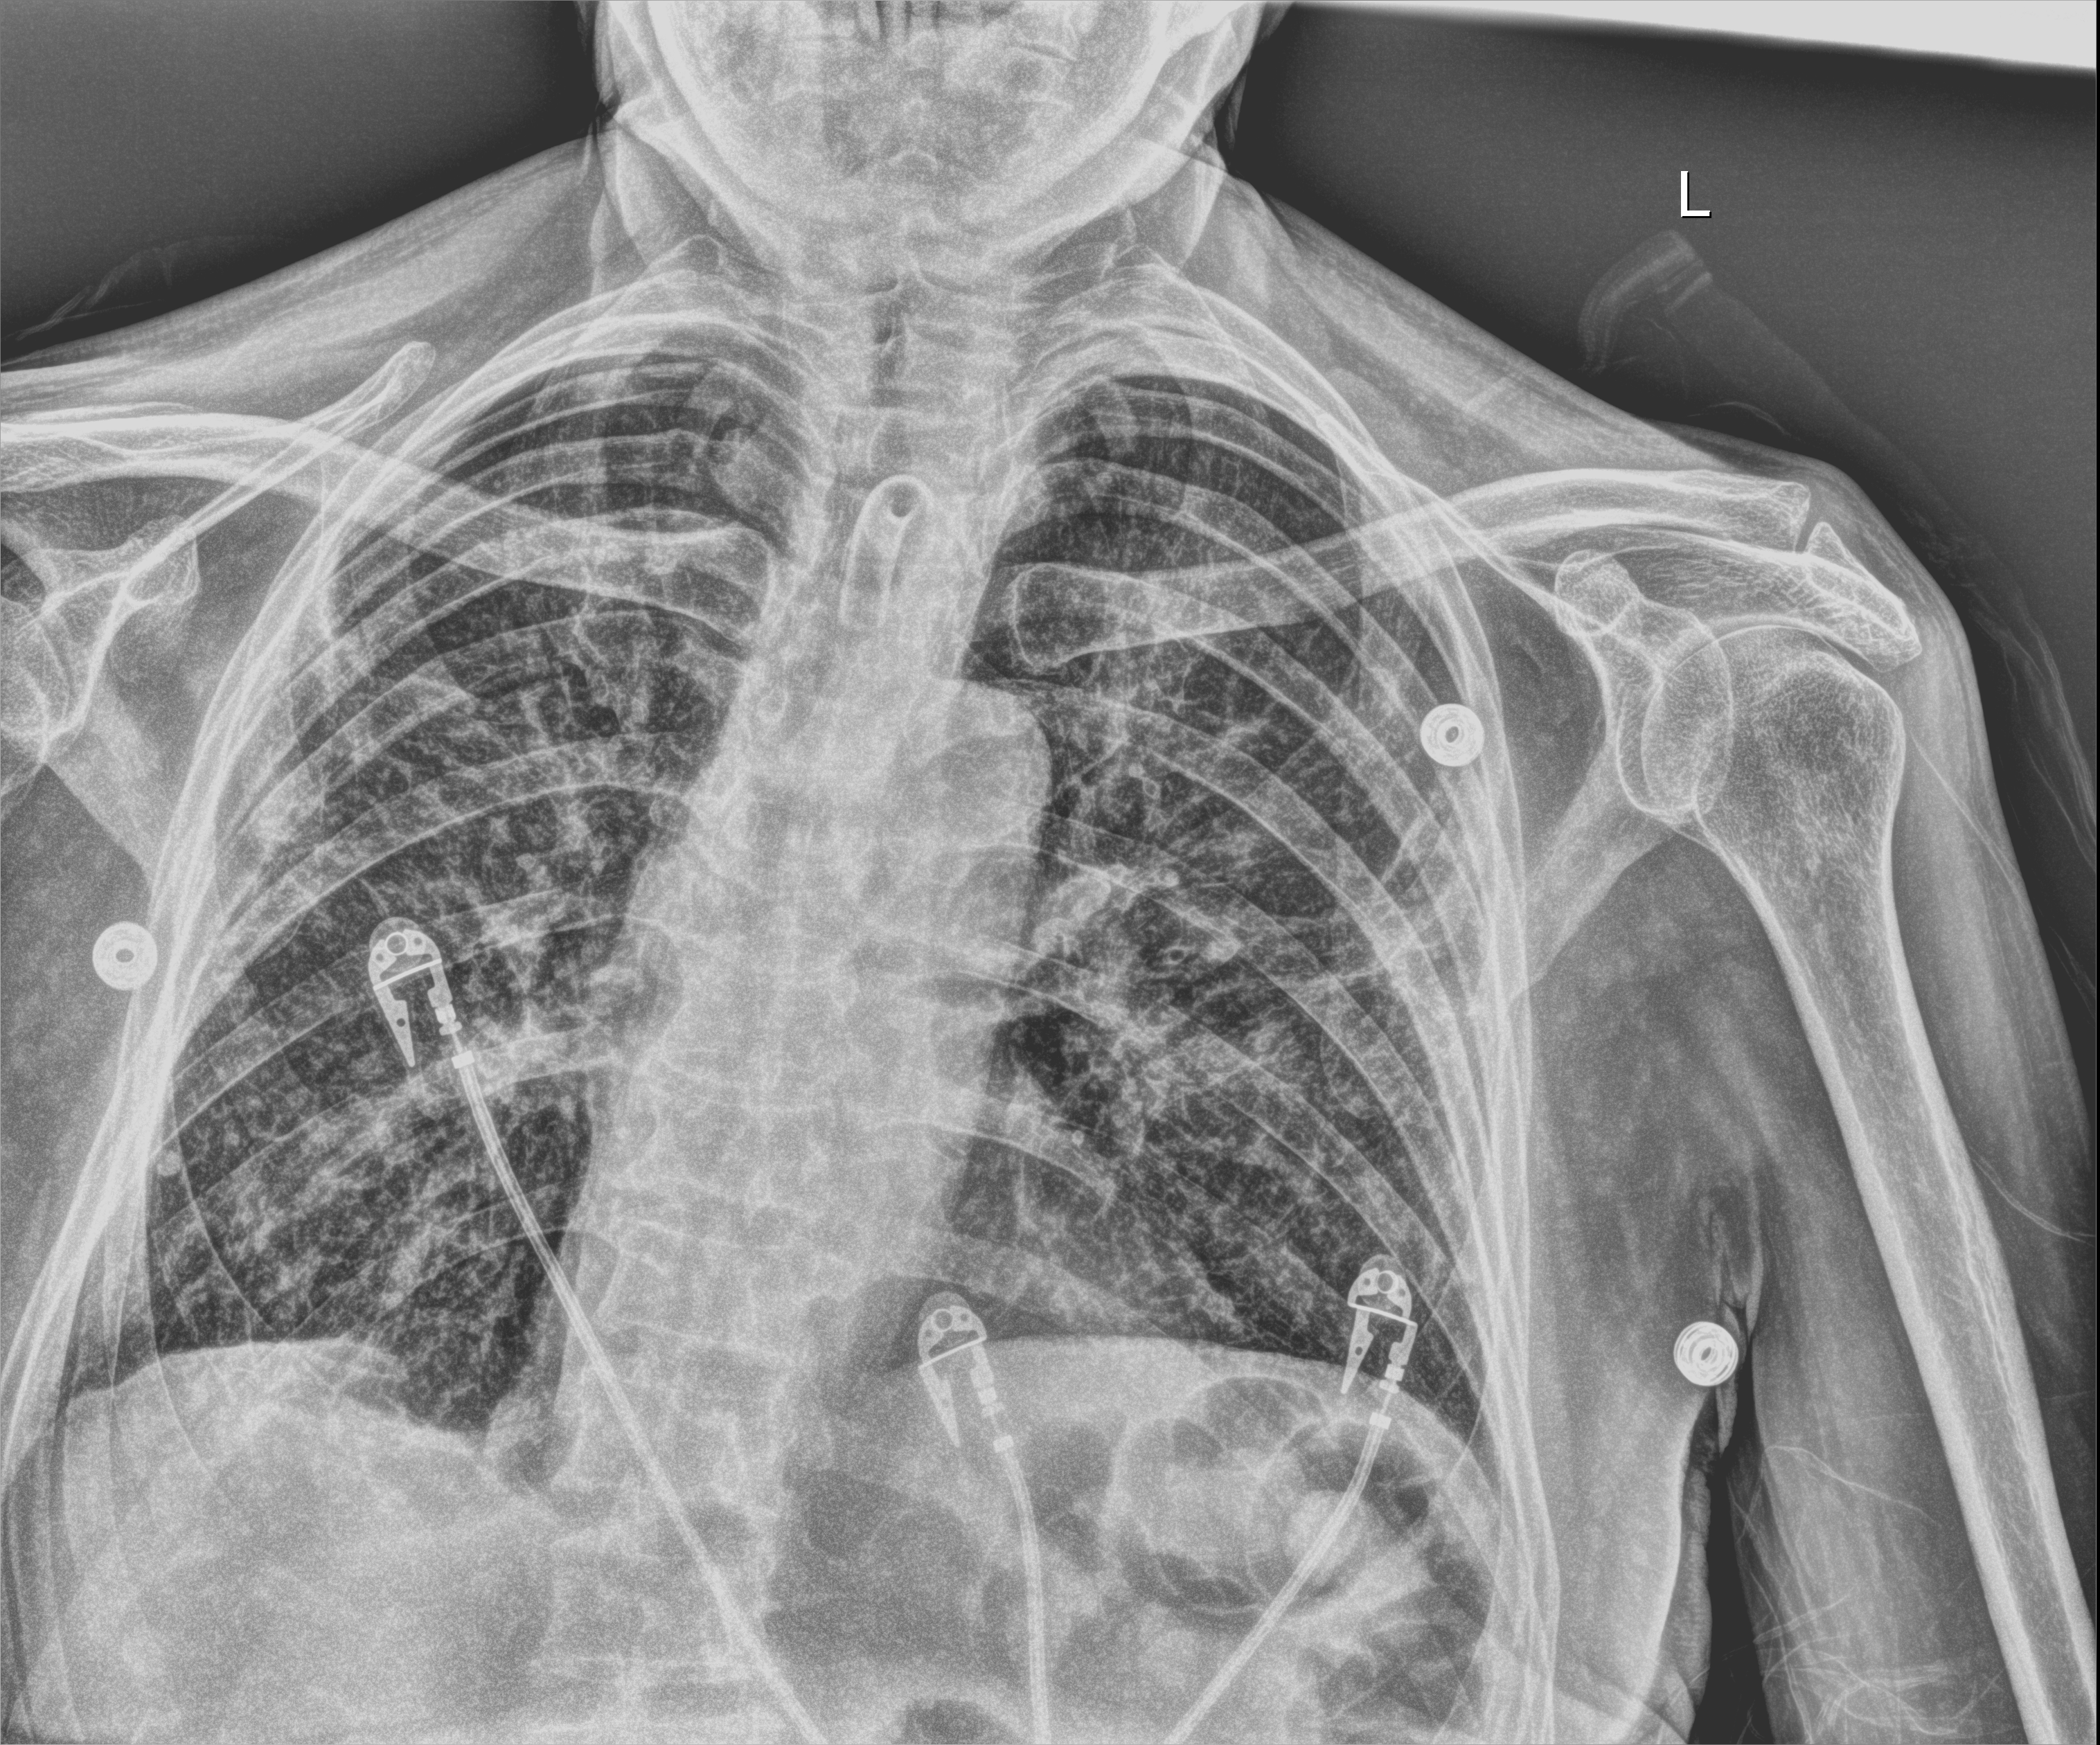
Bedside chest radiograph (digital radiography), anteroposterior (AP) projection. Patient hospitalised with COVID-19; male, aged 75–90 years.
From the hospital-stay record, not from the radiograph (when in the stay this image was taken is not recorded): length of hospital stay: 70 days; mechanically ventilated during this hospital stay: yes.